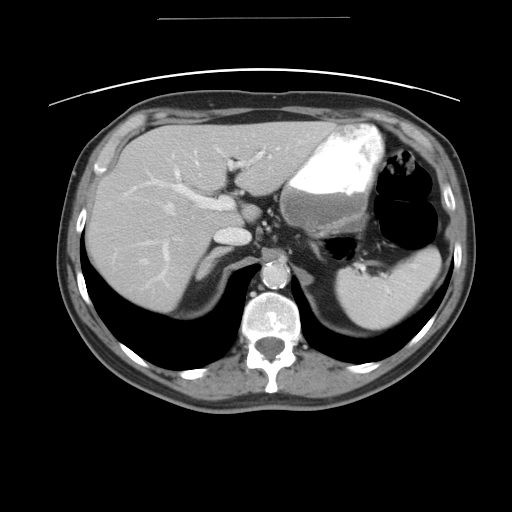
Contrast-enhanced abdominal CT, one axial slice. Slice 32 of 49 in the series (ordered by position). 120 kVp. Intravenous contrast given. Soft-tissue window (W 400 / L 40 HU). 5 mm slice thickness. 512 × 512 image matrix, field of view 413 × 413 mm. Male patient, age 57 years. Case-level facts recorded for this patient, not image findings: diagnosis: colorectal cancer liver metastases, imaged before liver resection; multiple liver metastases: yes; largest metastasis: 4 cm; disease in both lobes: no.
Structures marked on this image (manually delineated by an expert):
- hepatic veins: bounding box [x1, y1, x2, y2] px = [141, 155, 270, 263]
- liver: [86, 121, 334, 310]
- planned liver remnant (the part of the liver to remain after resection): [208, 121, 334, 228]
- portal vein (with intrahepatic branches): [122, 145, 278, 277]